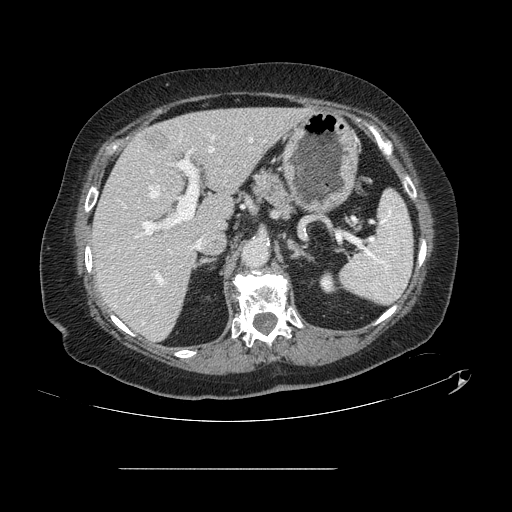
Contrast-enhanced abdominal CT, one axial slice. Position 79 of 148 along the scan axis. 120 kVp. Intravenous contrast given. Soft-tissue window (W 400 / L 40 HU). 2.5 mm slice thickness. 512 × 512 image matrix, field of view 439 × 439 mm. Female patient, age 75 years. From the clinical record (not read from this slice): diagnosis: colorectal cancer liver metastases, imaged before liver resection; multiple liver metastases: no; largest metastasis: 2.4 cm.
Outlined on this slice (expert manual segmentation):
- hepatic veins: bounding box (x1, y1, x2, y2) in pixels: (150, 148, 214, 243)
- liver: (92, 108, 304, 341)
- planned liver remnant (the part of the liver to remain after resection): (93, 108, 303, 341)
- portal vein (with intrahepatic branches): (134, 137, 253, 284)
- liver metastasis: (145, 129, 170, 153)